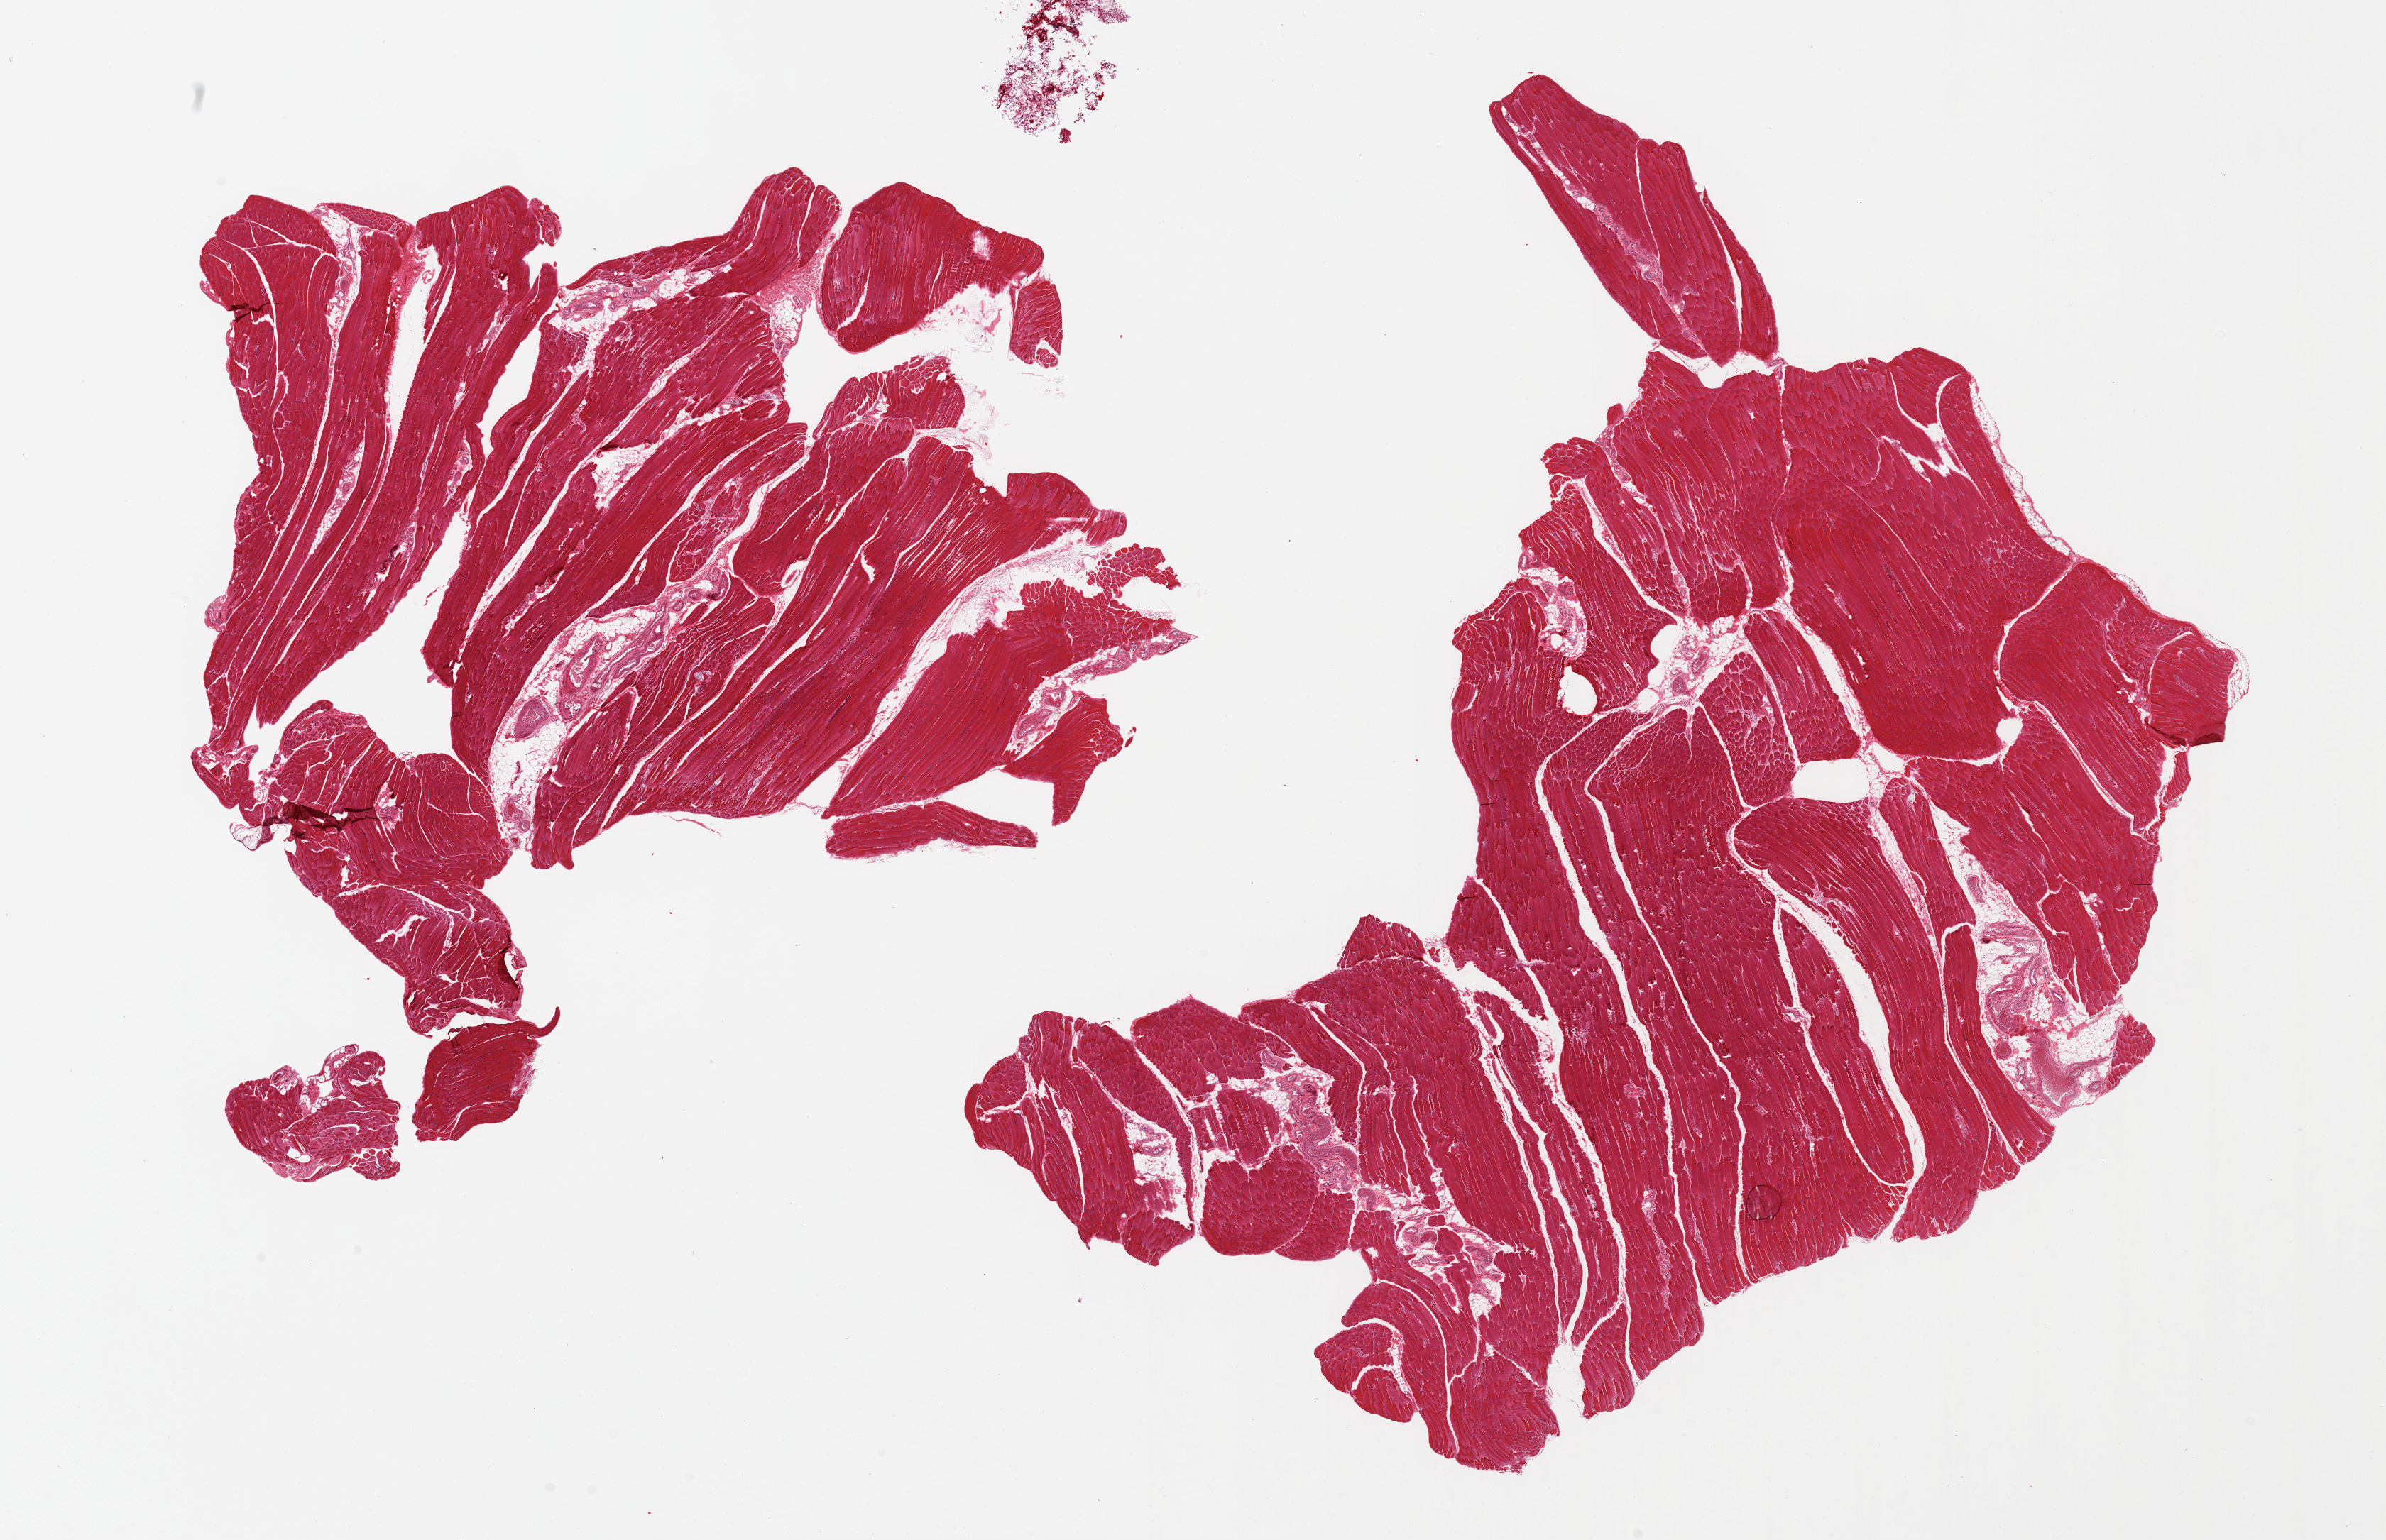
Digitized hematoxylin and eosin (H&E)-stained section — whole scanned area (about 26.6 x 17.2 mm) shown as a low-resolution overview; PAXgene-fixed, paraffin-embedded tissue; target tissue: skeletal muscle; donor tissue sample. Donor sex: male.
Review note (as recorded): 2 pieces. Focal atrophy.